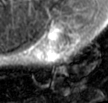
MRI of an extremity soft-tissue mass, one axial slice. Position 32 of 42 along the scan axis. T2-weighted fat-saturated. MR volume resampled by the dataset authors to the PET/CT grid (not the native acquisition matrix). 3.27 mm slice thickness. 108 × 103 image matrix, field of view 105 × 101 mm. Male patient. Case-level facts recorded for this patient, not image findings: histological type: leiomyosarcoma; grade: intermediate; site of the primary tumour: left pelvis.
Outlined on this slice (expert contour drawn on MRI and transferred to this co-registered scan by the dataset authors):
- gross tumour volume (mass): bounding box (x1, y1, x2, y2) in pixels: (35, 23, 72, 63)